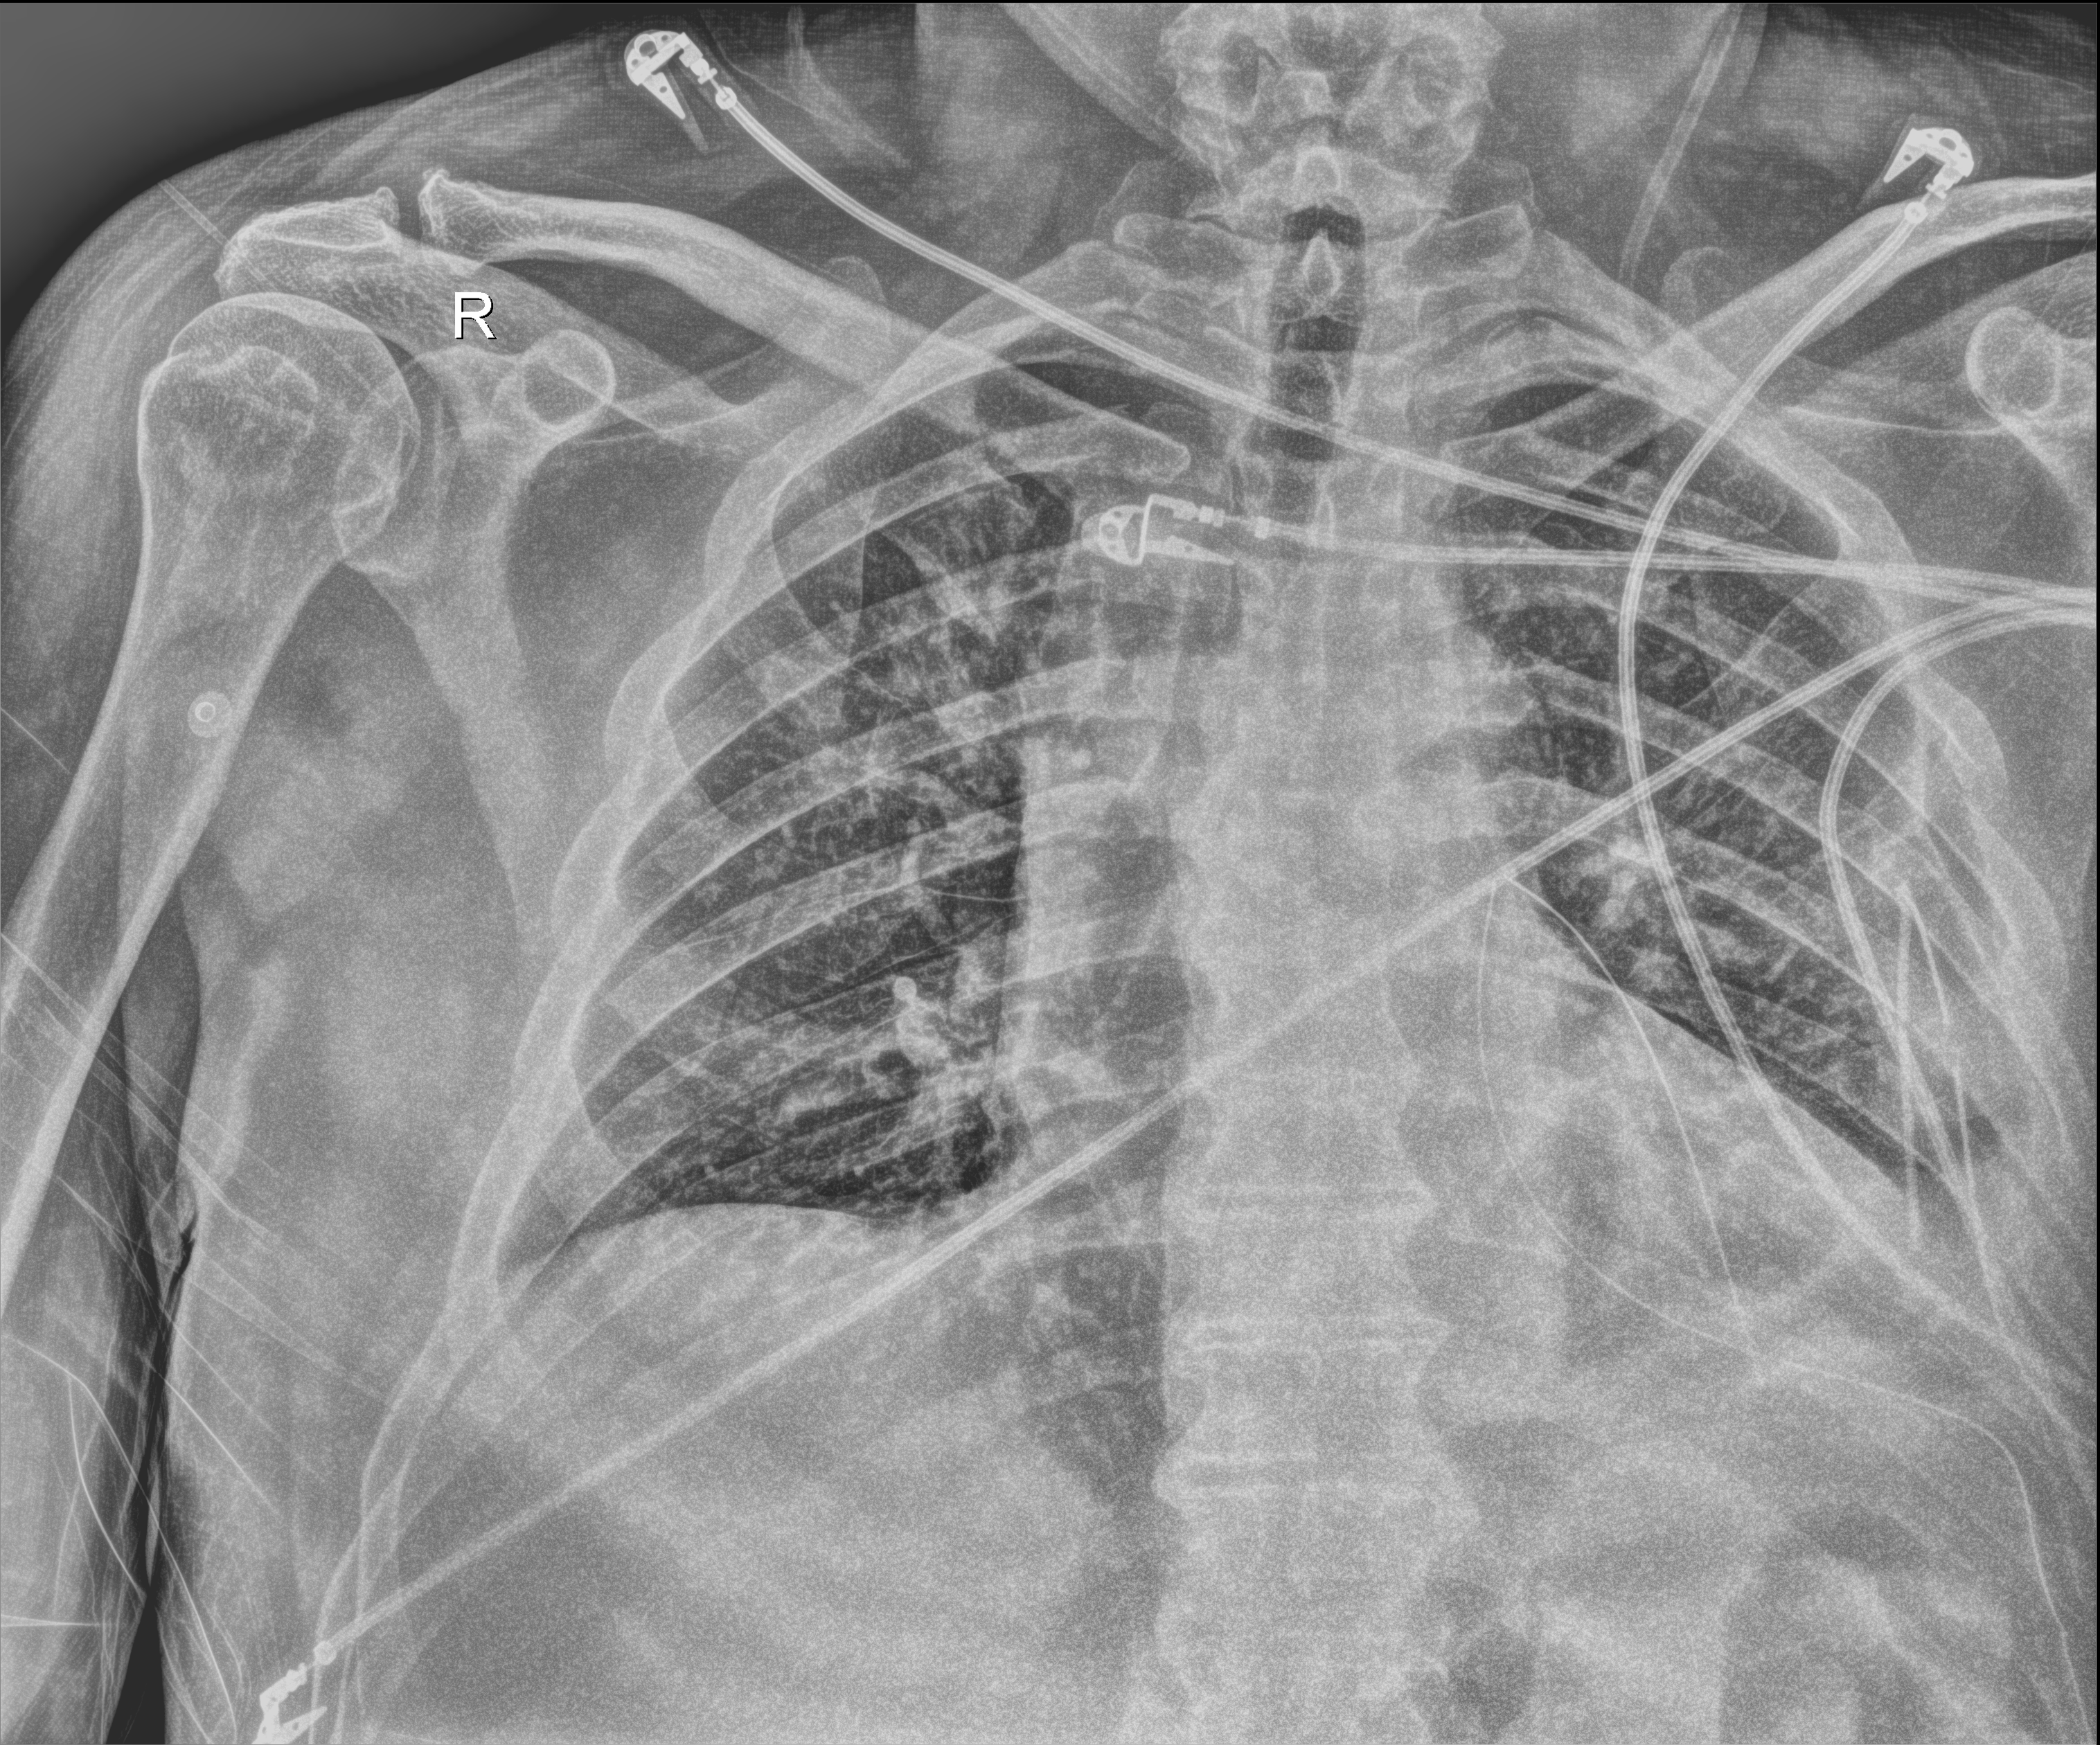
Portable chest radiograph; anteroposterior (AP) projection. Male patient hospitalised with COVID-19, age 18–59 years.
From the hospital-stay record, not from the radiograph (when in the stay this image was taken is not recorded):
- admitted to intensive care during this hospital stay: no
- length of hospital stay: 10 days
- mechanically ventilated during this hospital stay: no